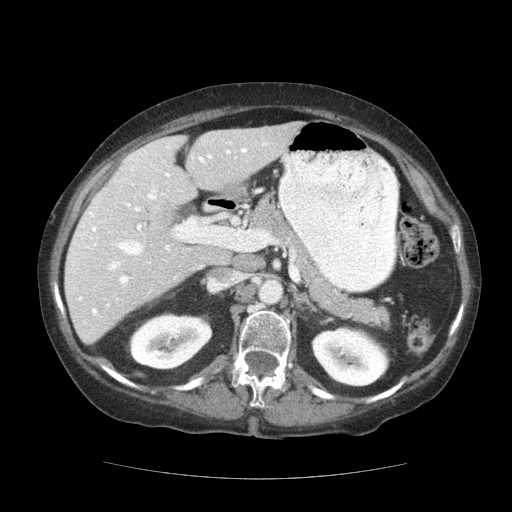
Contrast-enhanced abdominal CT (liver protocol), one axial slice; position 70 of 111 along the scan axis; reconstruction kernel STANDARD; 140 kVp; soft-tissue window (W 400 / L 40 HU); 2.5 mm slice thickness; 512 × 512 image matrix, field of view 360 × 360 mm. Case-level facts recorded for this patient, not image findings: diagnosis: hepatocellular carcinoma (patient treated with transarterial chemoembolisation; whether this scan precedes or follows treatment is not stated here); TNM stage (as recorded): Stage-I; Child-Pugh class: A; tumour differentiation: moderately-poorly differentiated; tumour nodularity: uninodular.
Annotated regions visible in this slice (semi-automatically segmented with operator editing):
- liver parenchyma outside the tumour (the mass and vessels are separate outlines, so this box may not span the whole liver): bounding box <64,122,300,344> (left, top, right, bottom; pixels)
- liver vessels: <77,142,268,315>